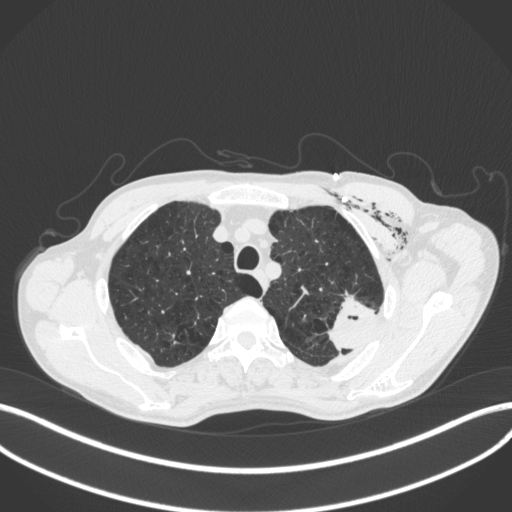
Chest CT, one axial slice. Slice 337 of 416 in the series (ordered by position). Reconstruction kernel B31f. Lung window (W 1500 / L -600 HU). 1 mm slice thickness. 512 × 512 image matrix, field of view 400 × 400 mm. Male patient, age 58 years. Case-level facts recorded for this patient, not image findings: clinical TNM (as recorded): T3 N0 M0.
Annotated regions visible in this slice (bounding box drawn by a radiologist):
- lung tumour (recorded histology: adenocarcinoma): bounding box (x1, y1, x2, y2) in pixels: (317, 291, 379, 353)